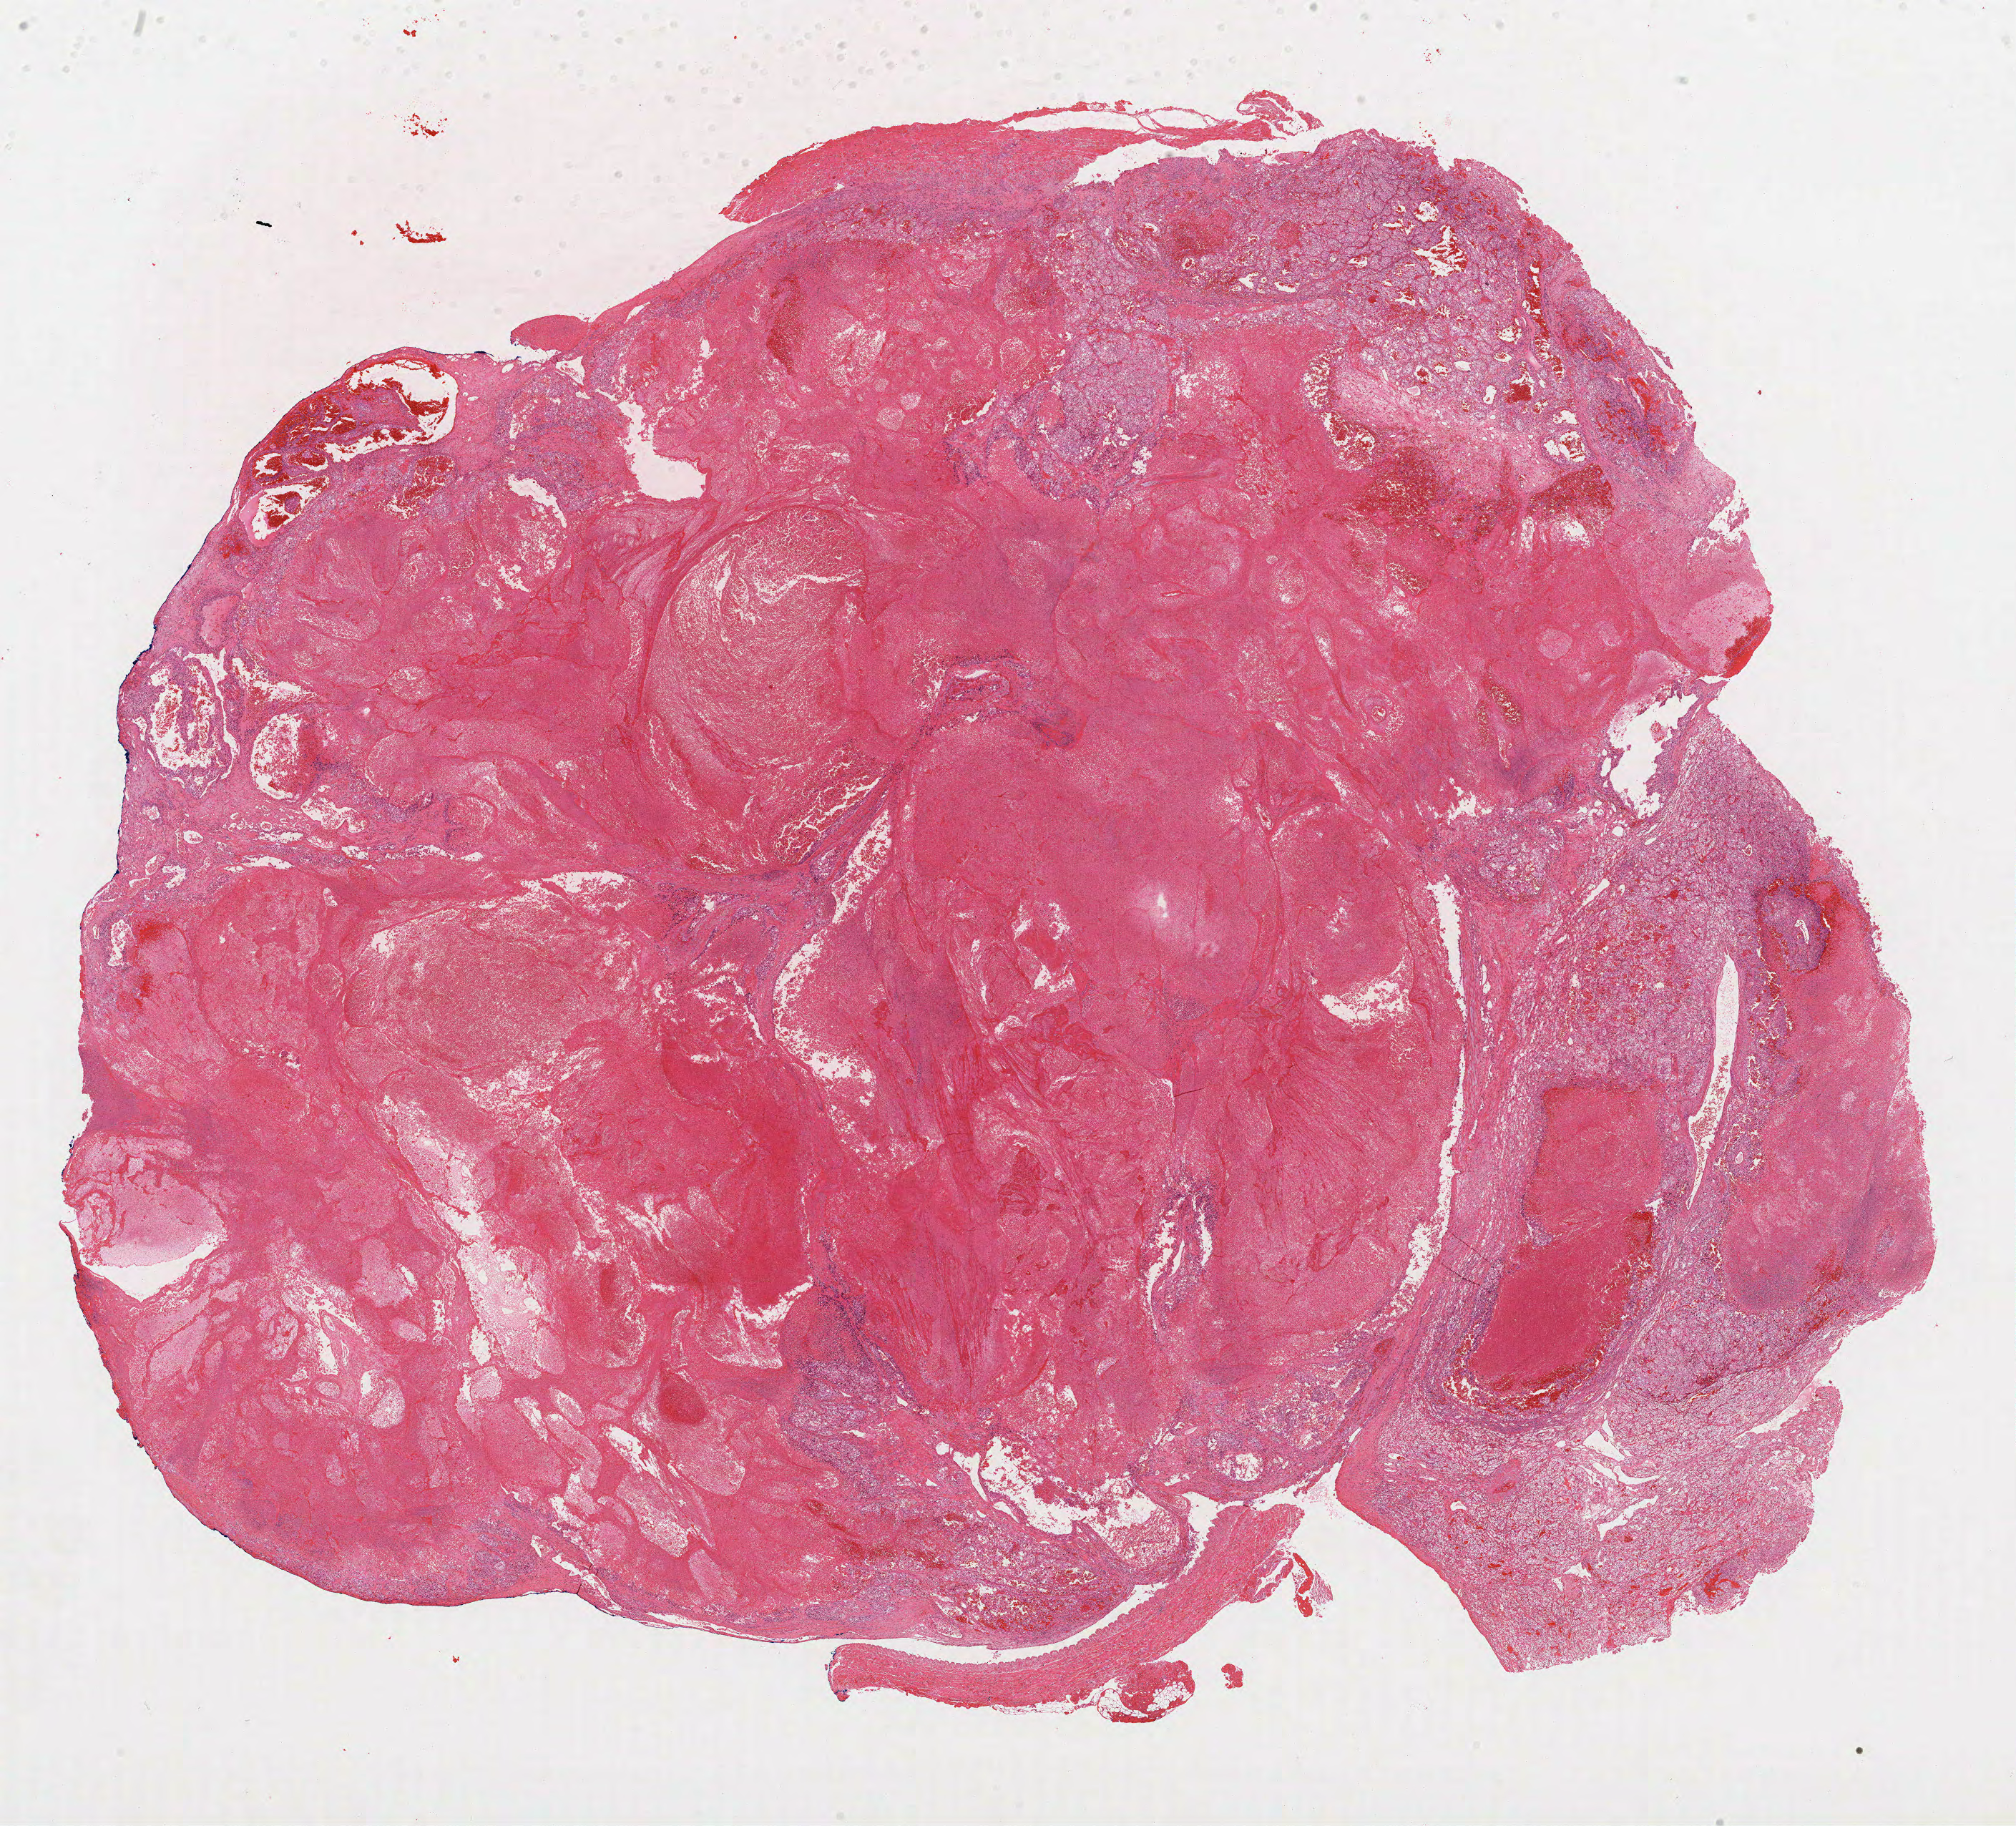
Digitized Hematoxylin and eosin (H&E) stained tissue section (whole slide), shown as a low-resolution overview of the whole scanned area (about 22.7 x 20.6 mm). Formalin-fixed paraffin-embedded (FFPE) diagnostic section. Sample: primary tumour, kidney. Patient: male, age at initial diagnosis 63 years. Histologic grade: G4 (undifferentiated).
• diagnosis: Clear cell adenocarcinoma, NOS
• AJCC pathologic stage: IV (6th edition)